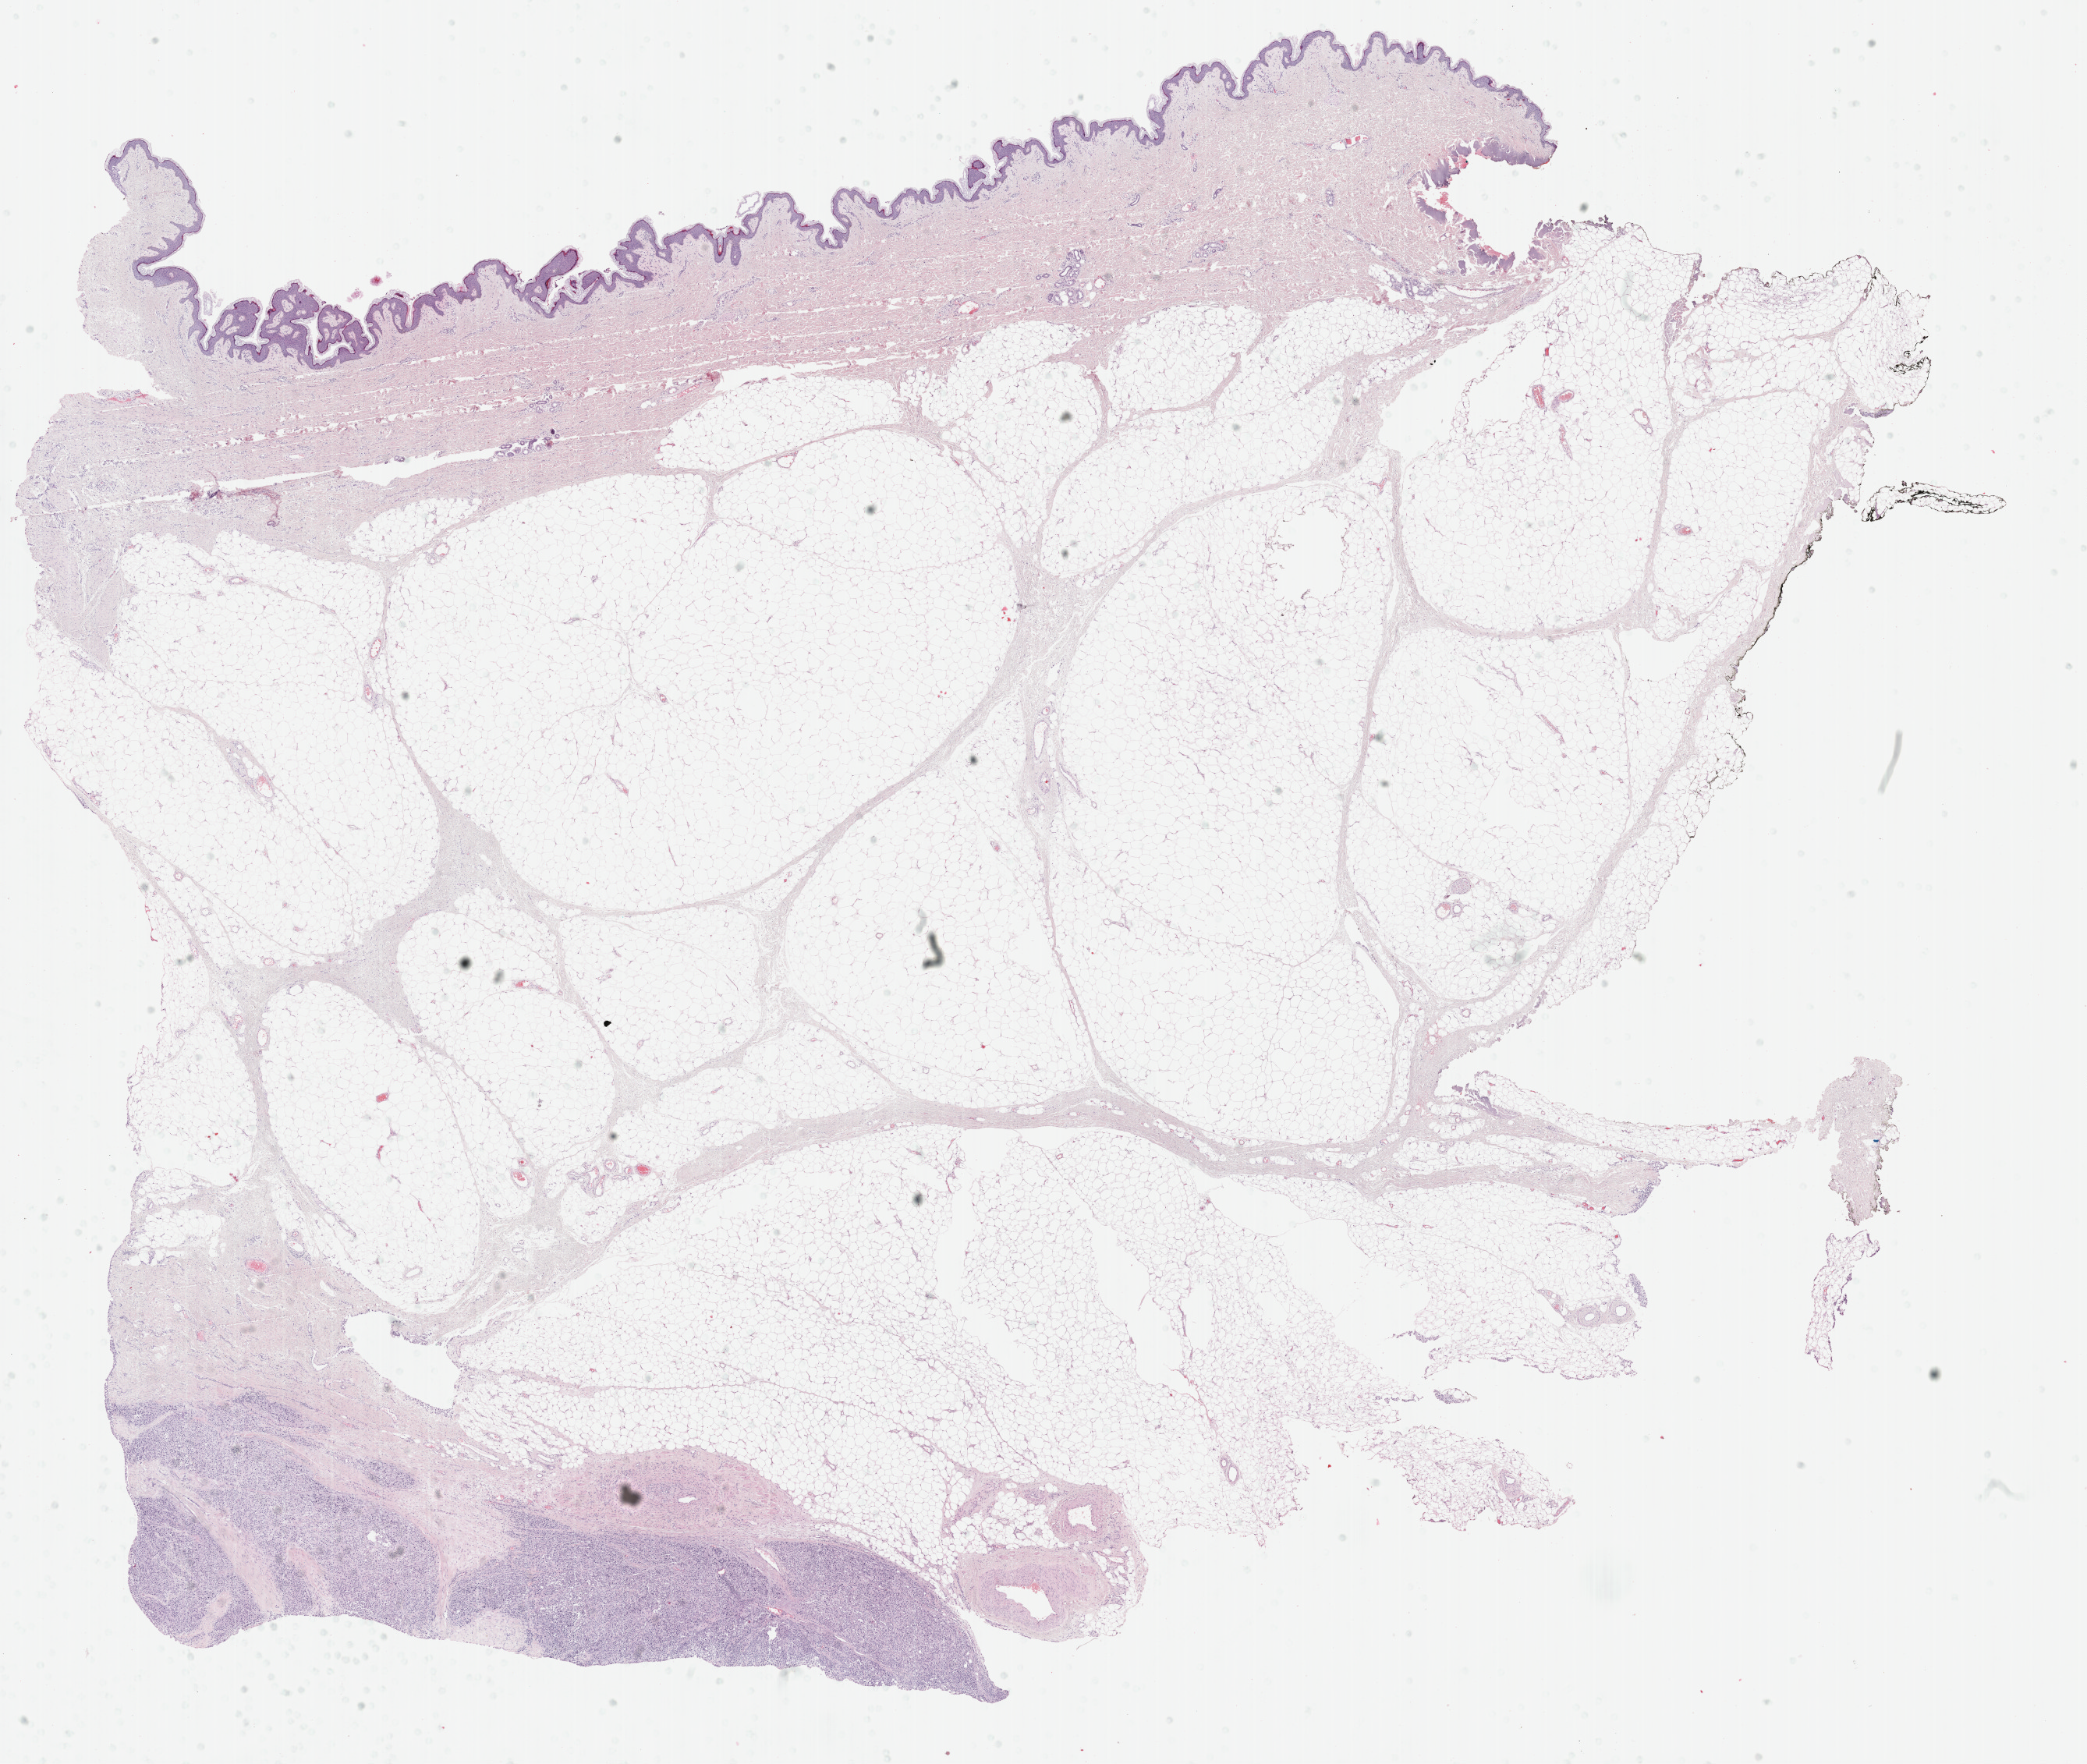
H&E whole-slide image — shown as a low-resolution overview of the whole scanned area (about 21.6 x 18.3 mm). Formalin-fixed paraffin-embedded (FFPE) diagnostic section. Sample: primary tumour, skin. Male, age 56 years at initial diagnosis.
- pathologic diagnosis: Malignant melanoma, NOS